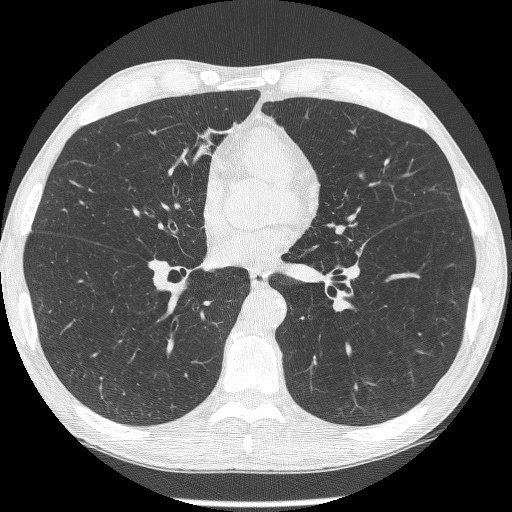
Axial slice from a low-dose chest CT screening exam, second screening round (one year after baseline), lung window (W 1500 / L -600 HU), lung (sharp) reconstruction kernel (BONE), slice 128 of 293 in the series, 512 × 512 image matrix, field of view 326 × 326 mm. Male, age 62 years at enrolment. Former smoker at enrolment.
Lesion marked by an expert reader, bounding box (x1, y1, x2, y2) in pixels: (322, 216, 371, 264). The screening reader recorded 2 non-calcified nodules or masses ≥4 mm on this exam (lingula, lingula); which of them this box marks is not recorded. Official screen result: positive, other. Later outcome: lung cancer diagnosed 95 days after this screen — small cell carcinoma, NOS, left upper lobe, stage IIIA (AJCC 6th edition).